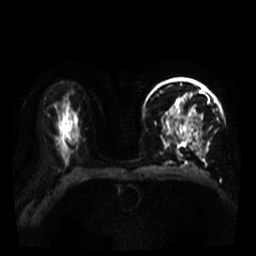
Breast MRI, one axial slice. Diffusion-weighted series; image 2 of 4 stored at this slice position (different b-values; order by instance number). 3 T. 256 × 256 image matrix, field of view 320 × 320 mm. Female patient.
Outlined on this slice (expert manual segmentation):
- tumour on diffusion-weighted imaging: bounding box [x1, y1, x2, y2] px = [191, 112, 201, 140]